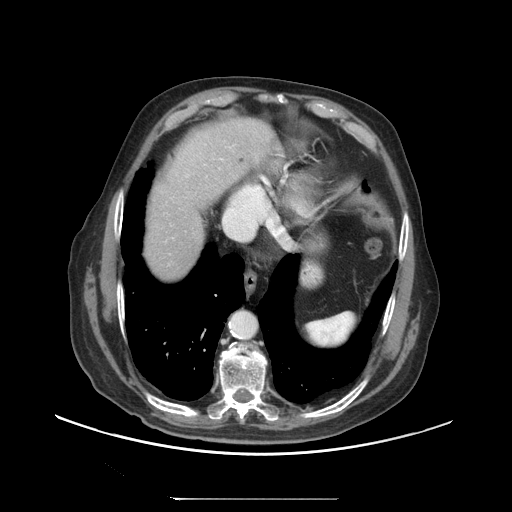
Contrast-enhanced abdominal CT (liver protocol), one axial slice. Position 85 of 97 along the scan axis. Soft-tissue window (W 400 / L 40 HU). 512 × 512 image matrix, field of view 450 × 450 mm. From the clinical record (not read from this slice): diagnosis: hepatocellular carcinoma (patient treated with transarterial chemoembolisation; whether this scan precedes or follows treatment is not stated here); TNM stage (as recorded): Stage-IIIC; Child-Pugh class: A; tumour differentiation: well differentiated.
Annotated regions visible in this slice (semi-automatically segmented with operator editing):
- abdominal aorta: bounding box <231,311,256,338> (left, top, right, bottom; pixels)
- liver parenchyma outside the tumour (the mass and vessels are separate outlines, so this box may not span the whole liver): <144,169,233,280>